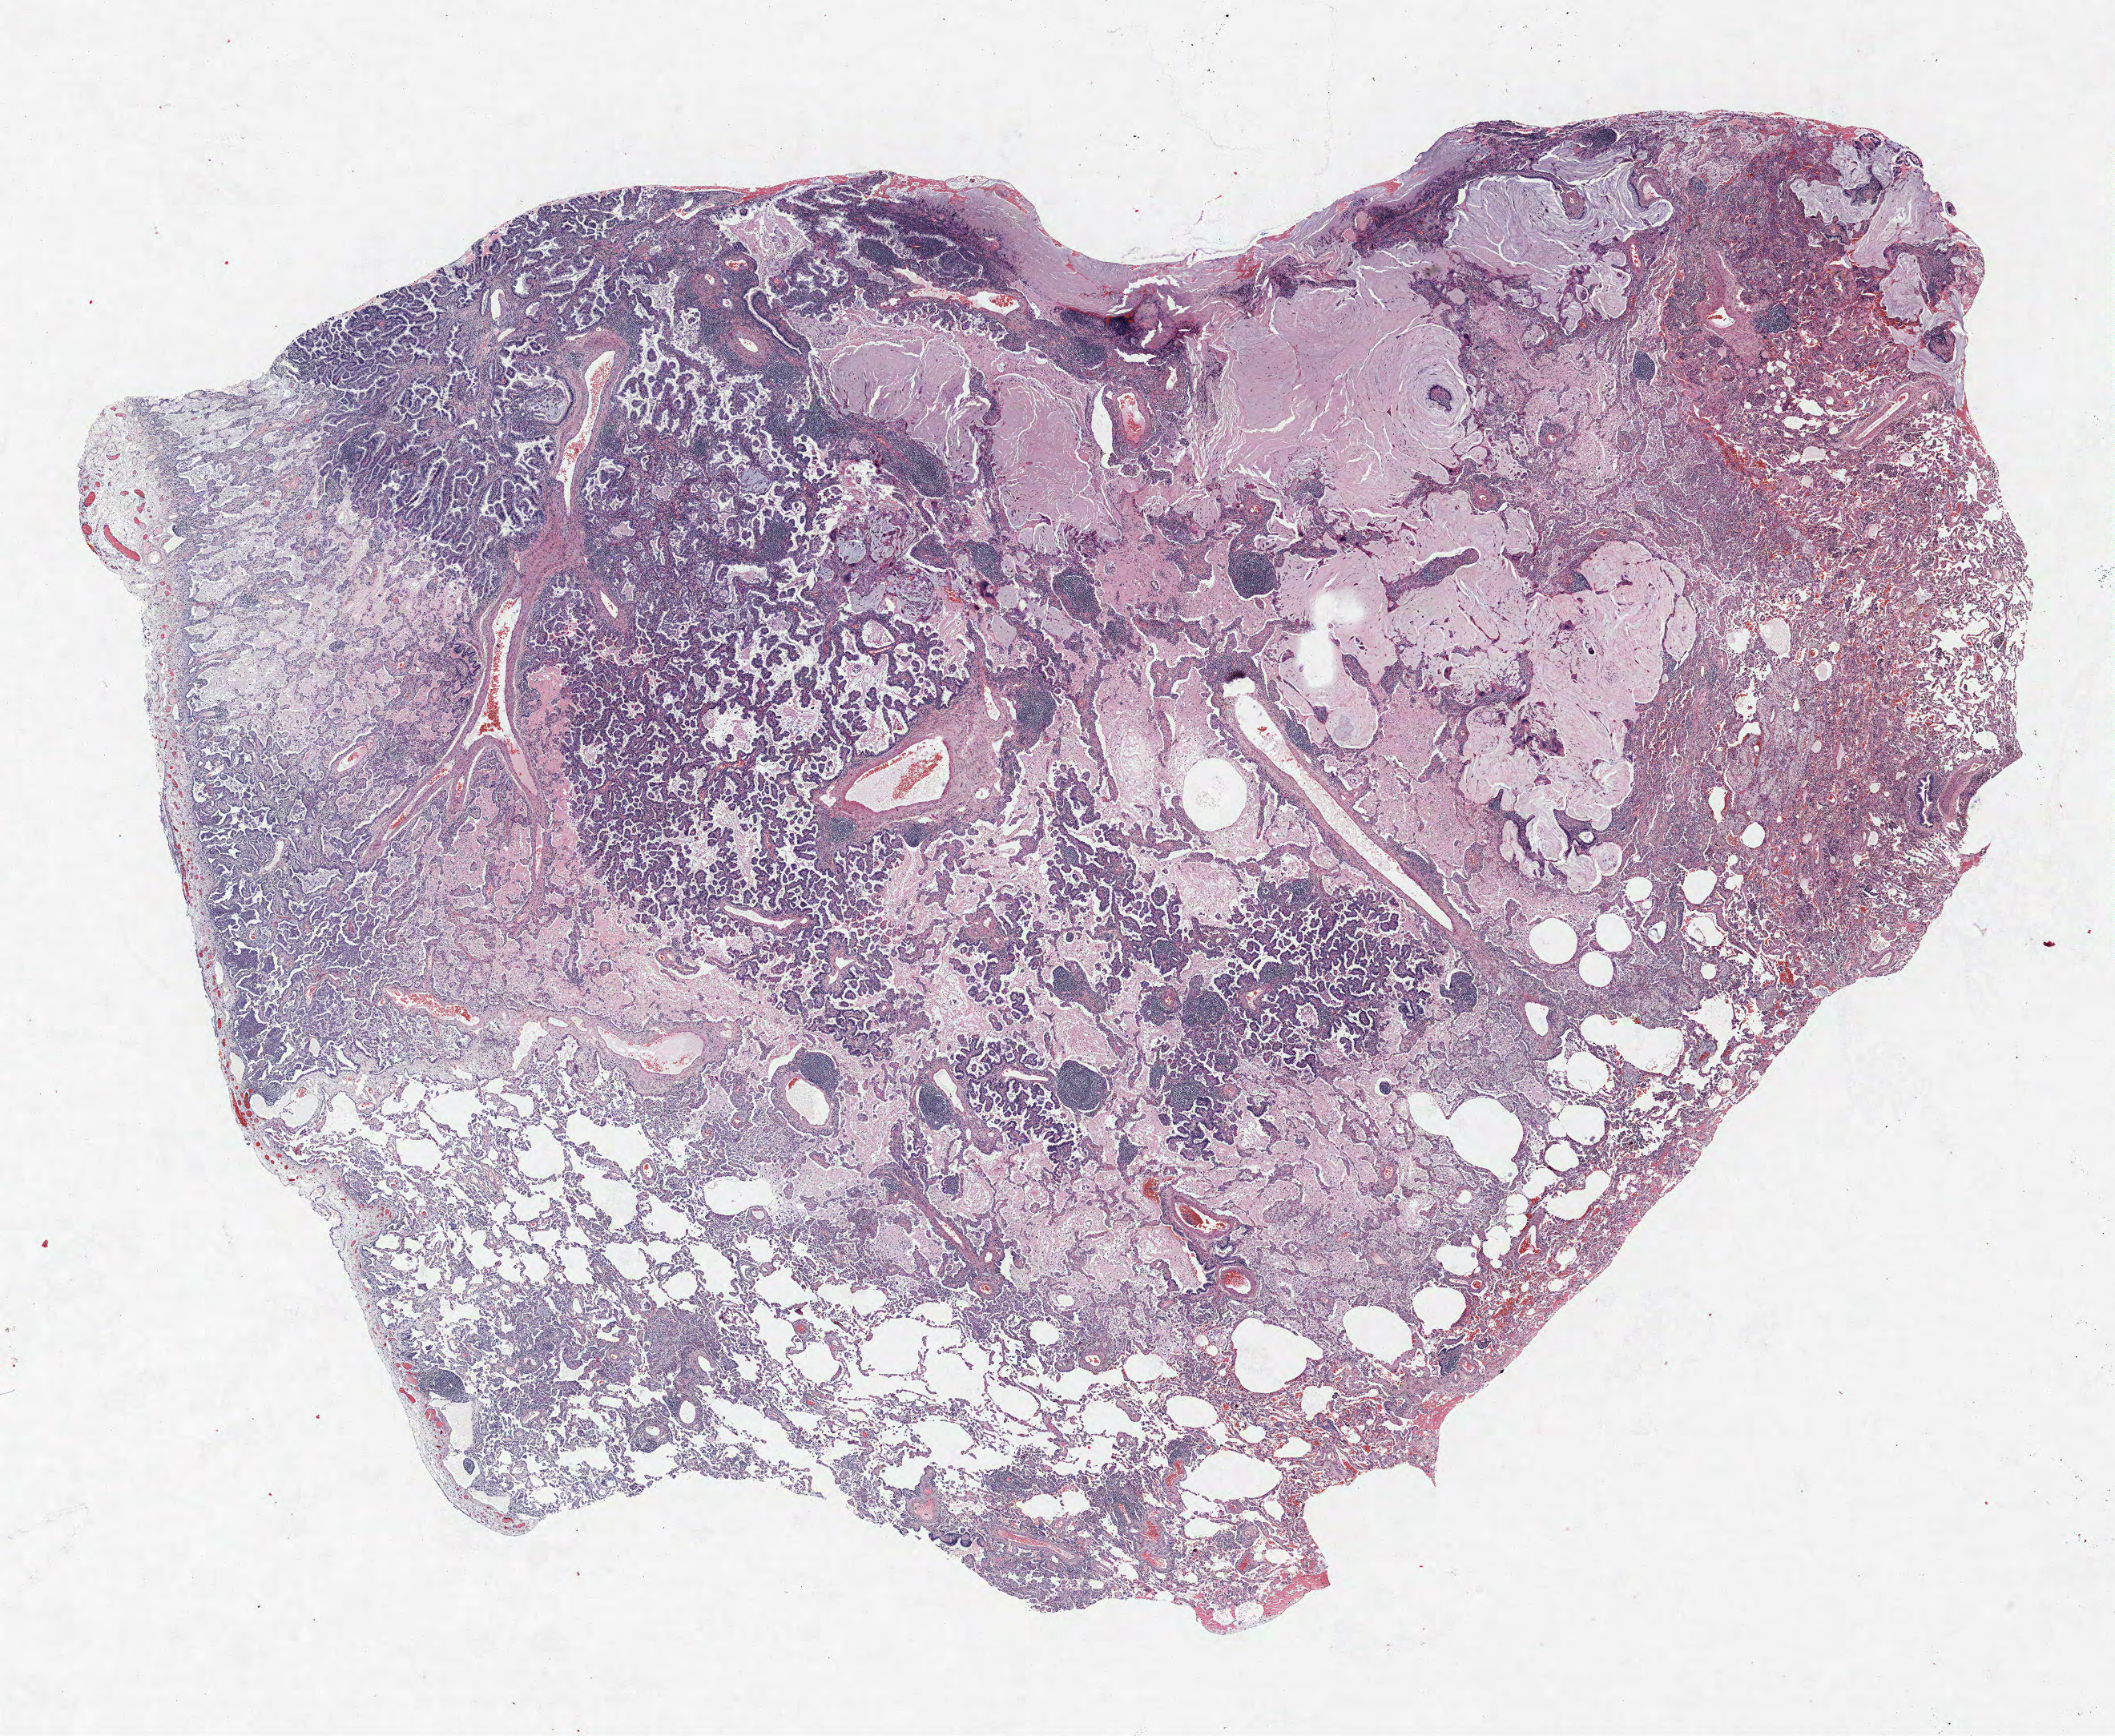
Whole-slide histology image, Hematoxylin and eosin (H&E) stained — whole scanned area (about 21.1 x 17.3 mm) shown as a low-resolution overview, formalin-fixed paraffin-embedded (FFPE) section, lung. Female patient, aged 68 at enrolment. Current smoker at enrolment. Grade: well differentiated (G1).
* participant's lung-cancer diagnosis: Adenocarcinoma, NOS
* primary tumour location (clinical record): right lower lobe
* stage (AJCC 6th edition): IA
* ICD-O-3 topography: lower lobe of lung (C34.3)
* tumour size (pathology): 25 mm